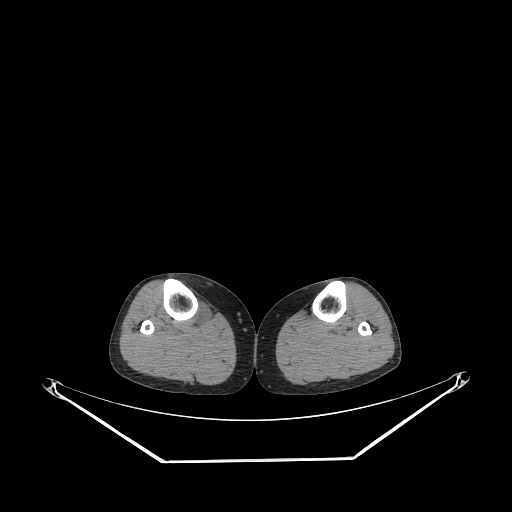
CT of an extremity soft-tissue mass (from a PET/CT study), one axial slice; position 151 of 267 along the scan axis; reconstruction kernel STANDARD; 140 kVp; soft-tissue window (W 400 / L 40 HU); 3.75 mm slice thickness; 512 × 512 image matrix, field of view 500 × 500 mm. Female patient. From the clinical record (not read from this slice): histological type: undifferentiated – high grade; grade: high; site of the primary tumour: right thigh.
Annotated regions visible in this slice (expert contour drawn on MRI and transferred to this co-registered scan by the dataset authors):
- gross tumour volume (mass): bounding box (x1, y1, x2, y2) in pixels: (194, 301, 213, 327)